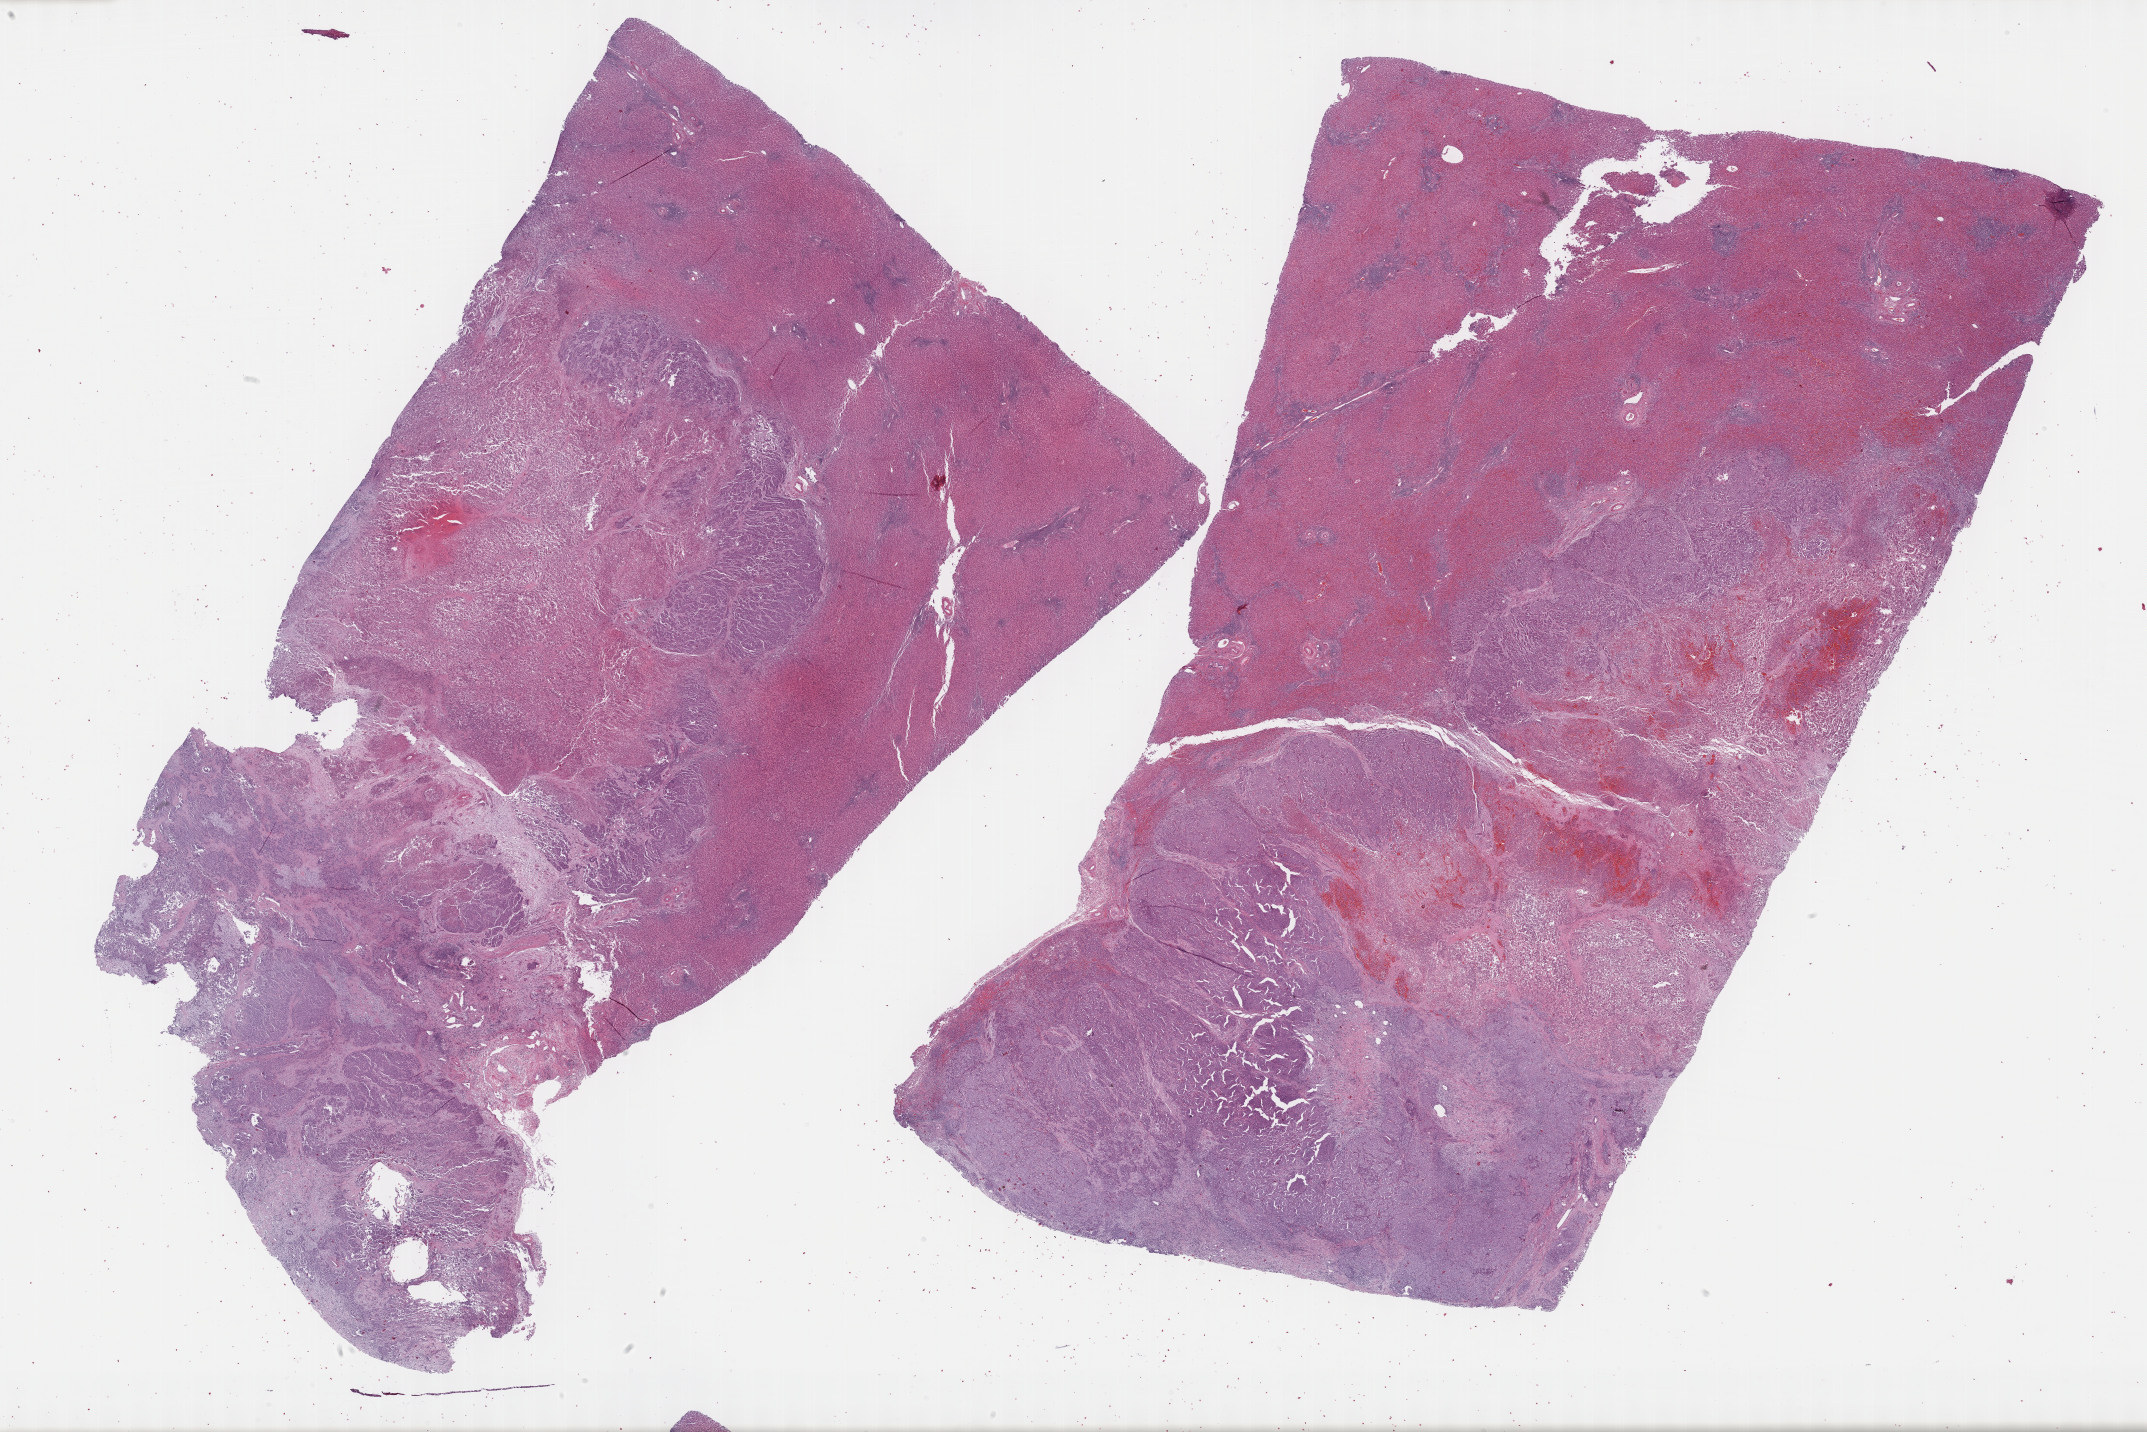
Whole-slide histology image, H&E, whole scanned area (about 34.7 x 23.2 mm) shown as a low-resolution overview, FFPE section, bile duct, primary tumour sample. Patient: female, age at initial diagnosis 31 years.
Diagnosis: Cholangiocarcinoma.